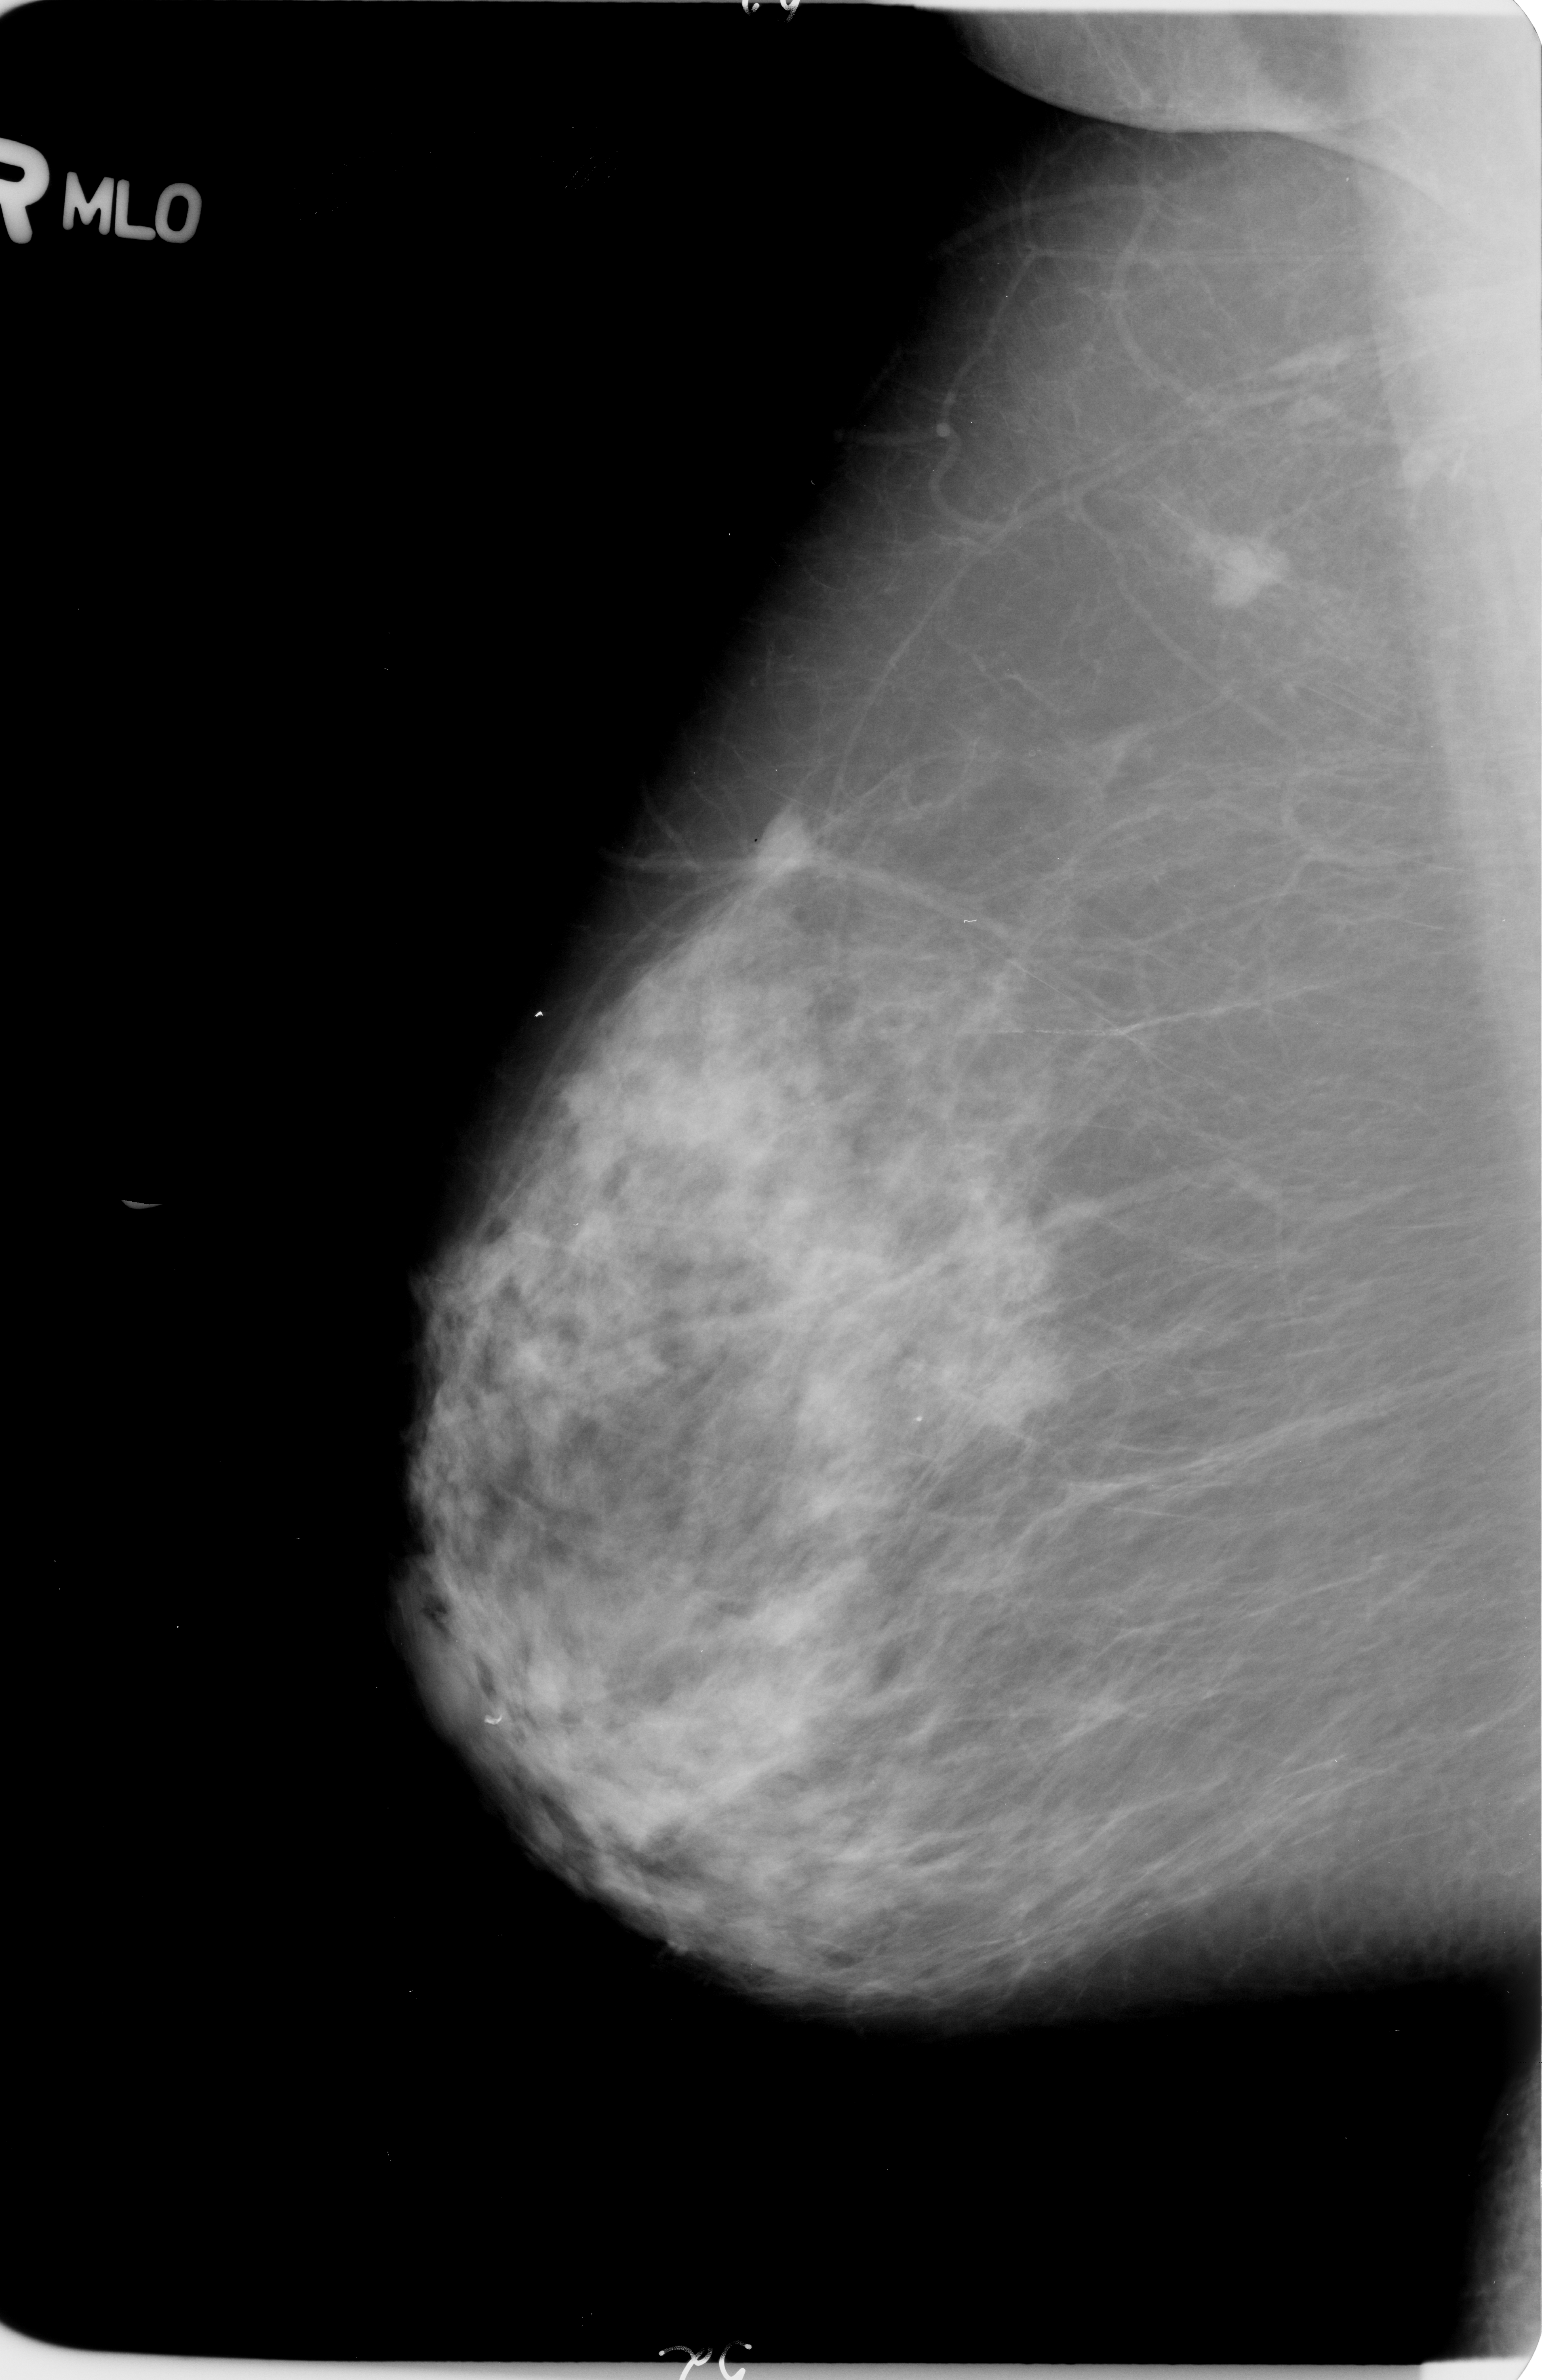
Digitized screen-film mammogram. Right breast. MLO view. 1542 × 2380 image matrix.
Expert-marked regions of interest on this image (one box per marked abnormality):
- mass, shape irregular, margins spiculated; BI-RADS assessment category 4; pathology result (as recorded, not read from the image): malignant: bounding box [x1, y1, x2, y2] px = [744, 800, 829, 891]